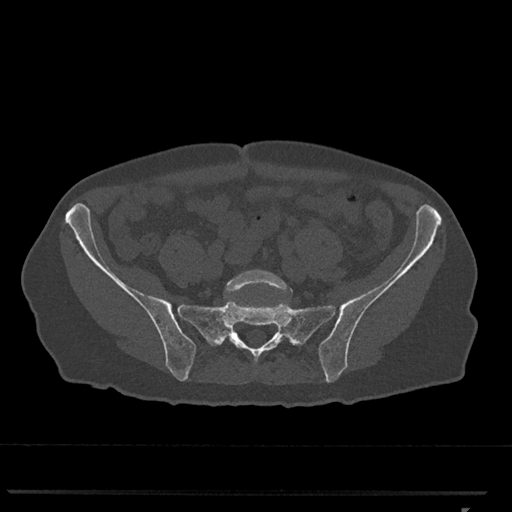
CT including the spine, one axial slice. Position 112 of 793 along the scan axis. Reconstruction kernel Br40s/3. 120 kVp. Bone window (W 1800 / L 400 HU). 0.5 mm slice thickness. 512 × 512 image matrix, field of view 380 × 380 mm. Female patient, age 62 years. Case-level facts recorded for this patient, not image findings: primary cancer: renal.
Annotated regions visible in this slice (semi-automatically segmented with operator editing):
- L5 vertebra: box from (x=225, y=269) to (x=293, y=296) px